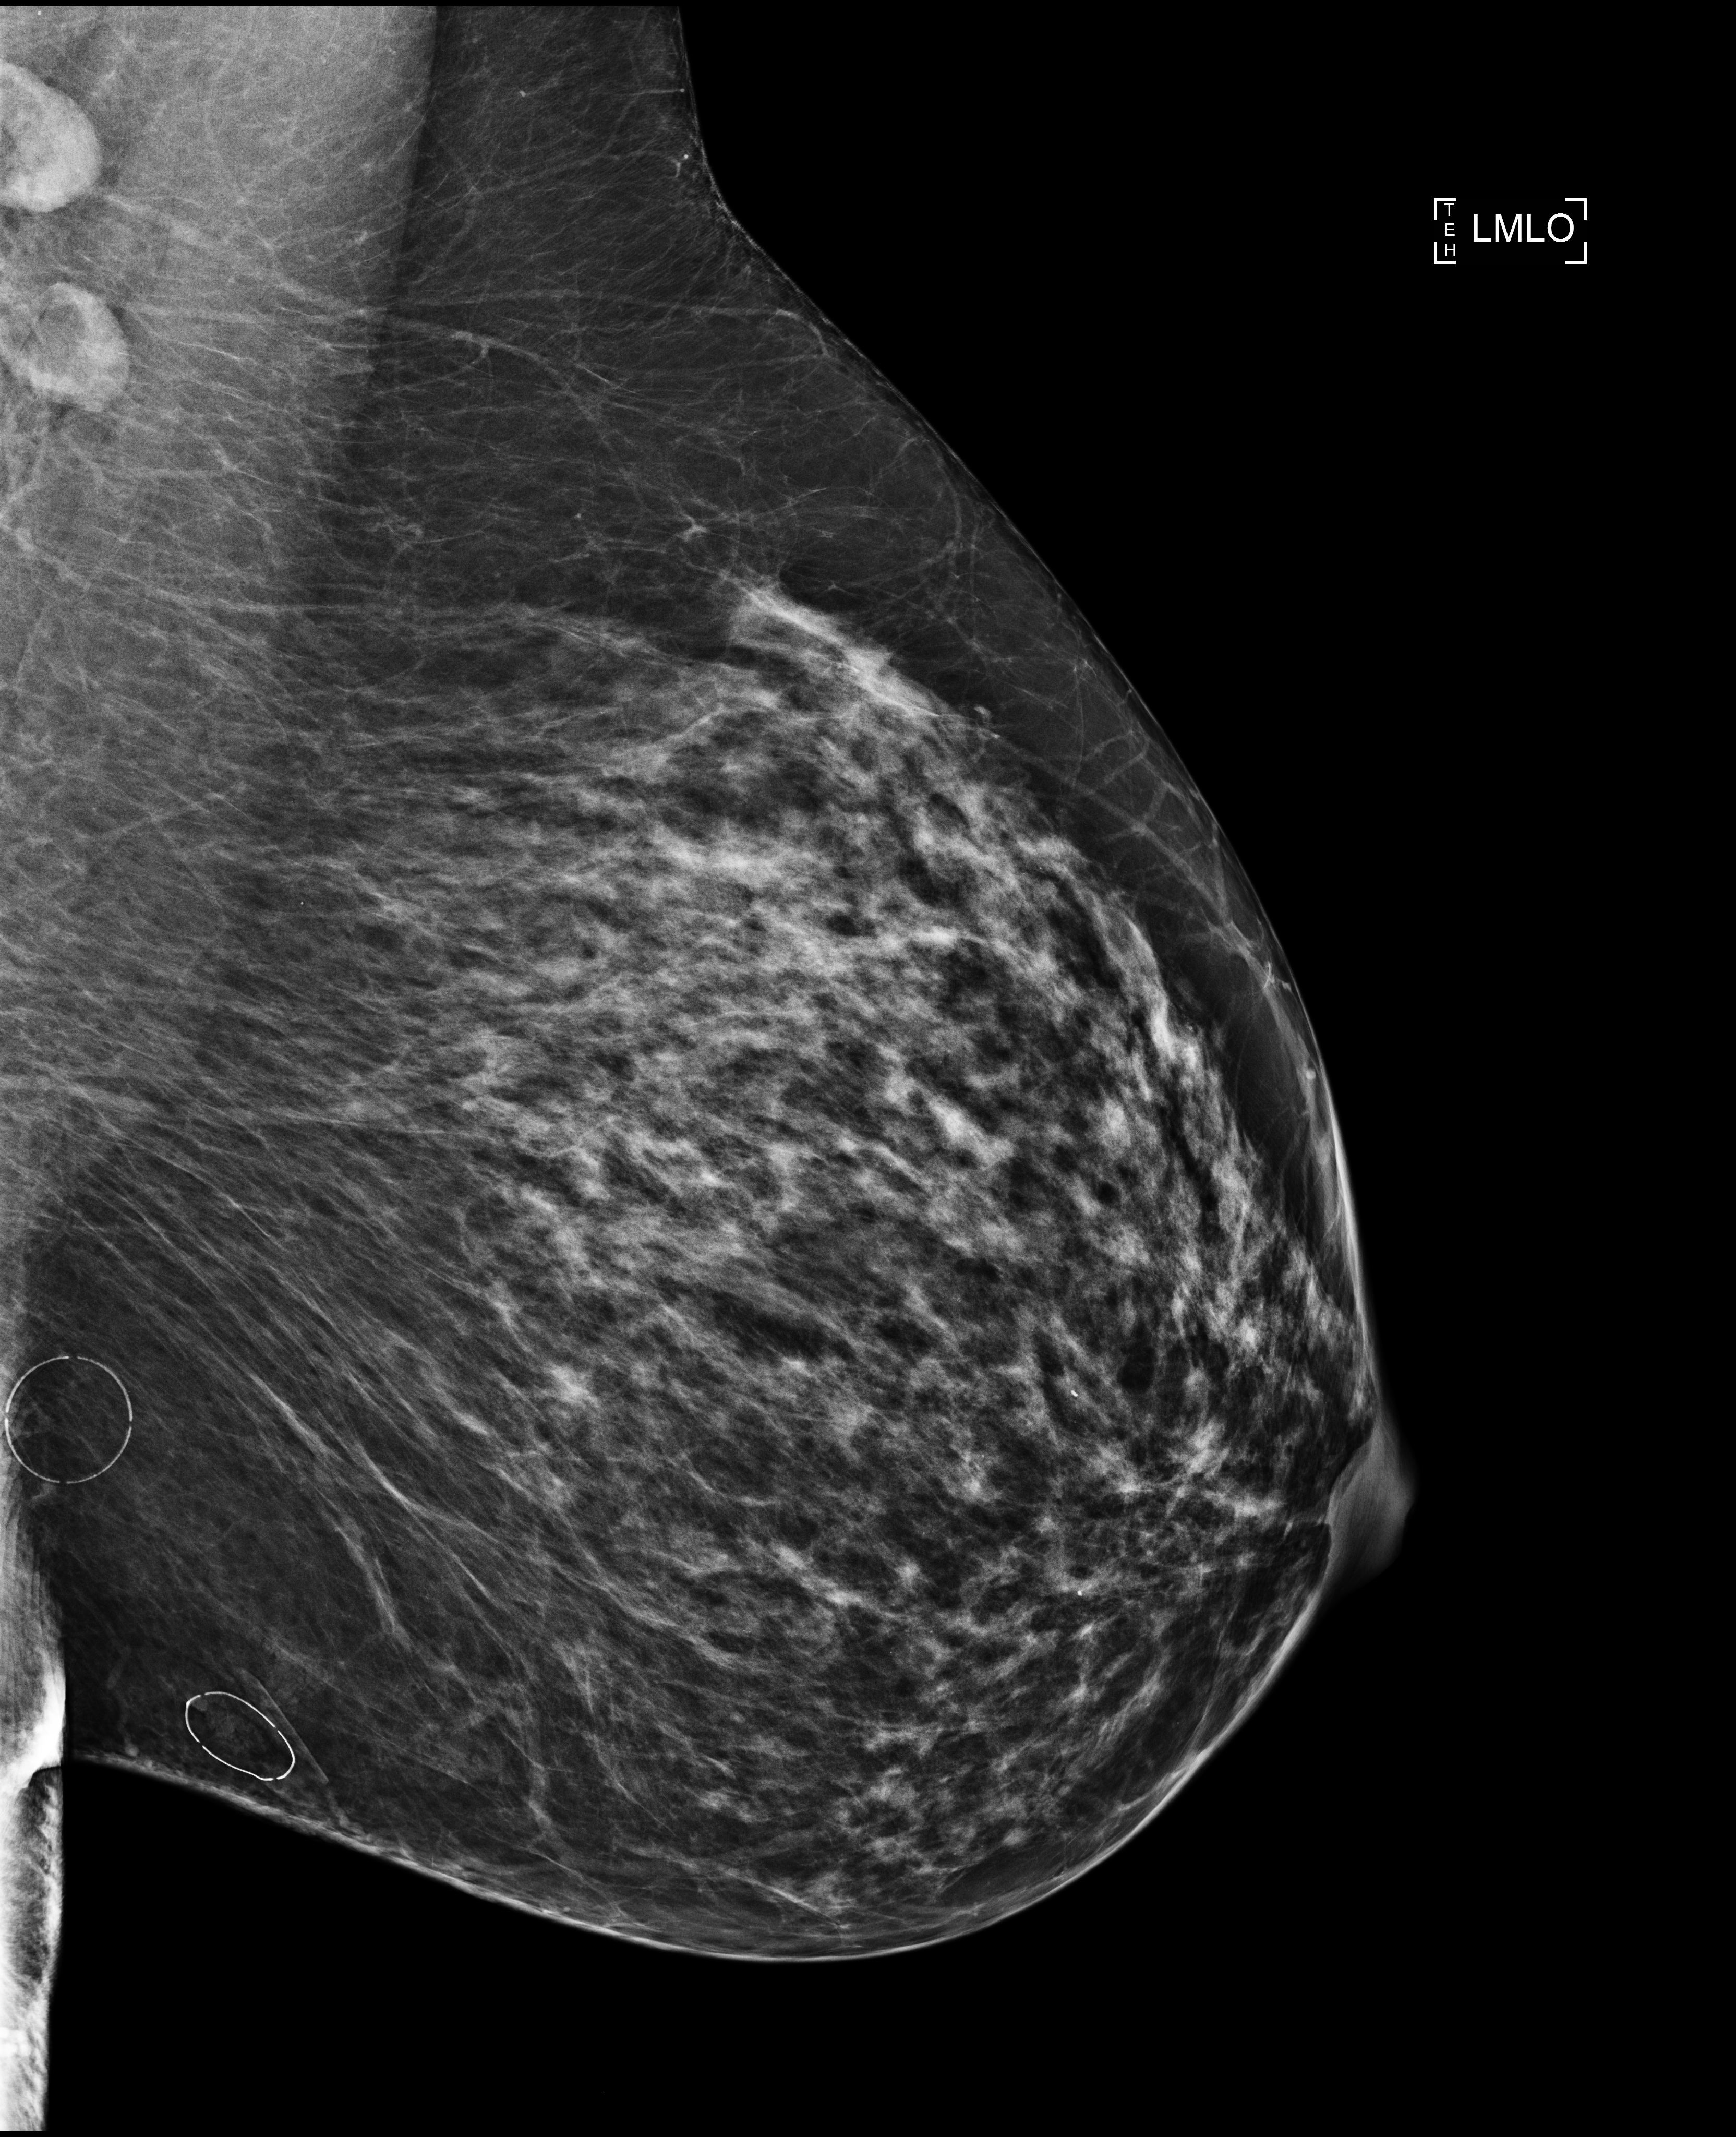
Full-field digital mammogram (FFDM), left breast, mediolateral oblique (MLO) view, screening examination, system: Selenia Dimensions. Patient: female, 61 years.
- breast density at the screening exam (both breasts): heterogeneously dense (BI-RADS density category c)
- final BI-RADS assessment for this screening round (tomosynthesis exam, both breasts): category 2
- recall: recalled for additional imaging after this screen